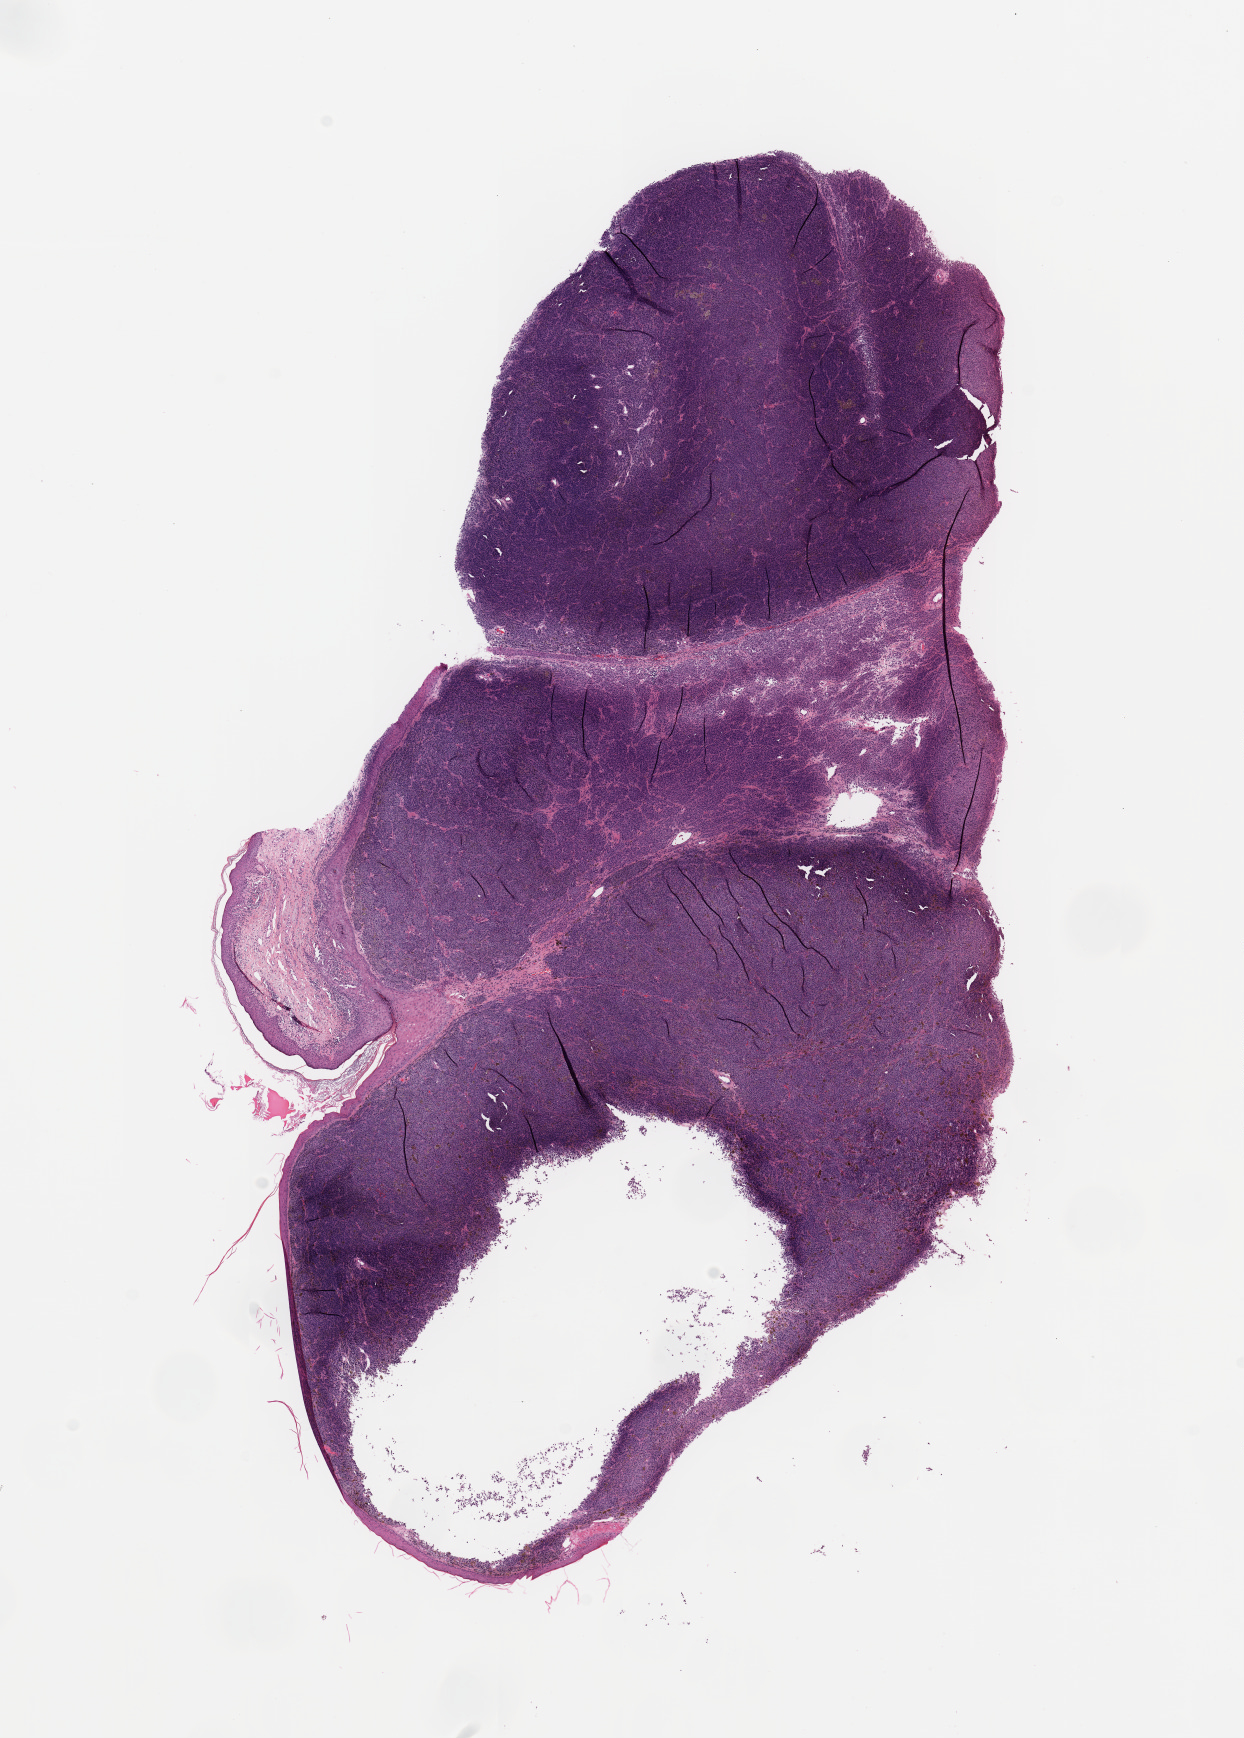
Hematoxylin and eosin (H&E) stained whole-slide image — whole scanned area (about 9.8 x 13.8 mm) shown as a low-resolution overview, tumour tissue sample, sampled site: skin. Female, 84 y/o. Composition of this section per pathologist review: tumour nuclei 95%, necrosis 0%.
Histologic diagnosis: Malignant melanoma, NOS. Primary tumour site (as recorded): extremities. AJCC pathologic stage: IIIC.